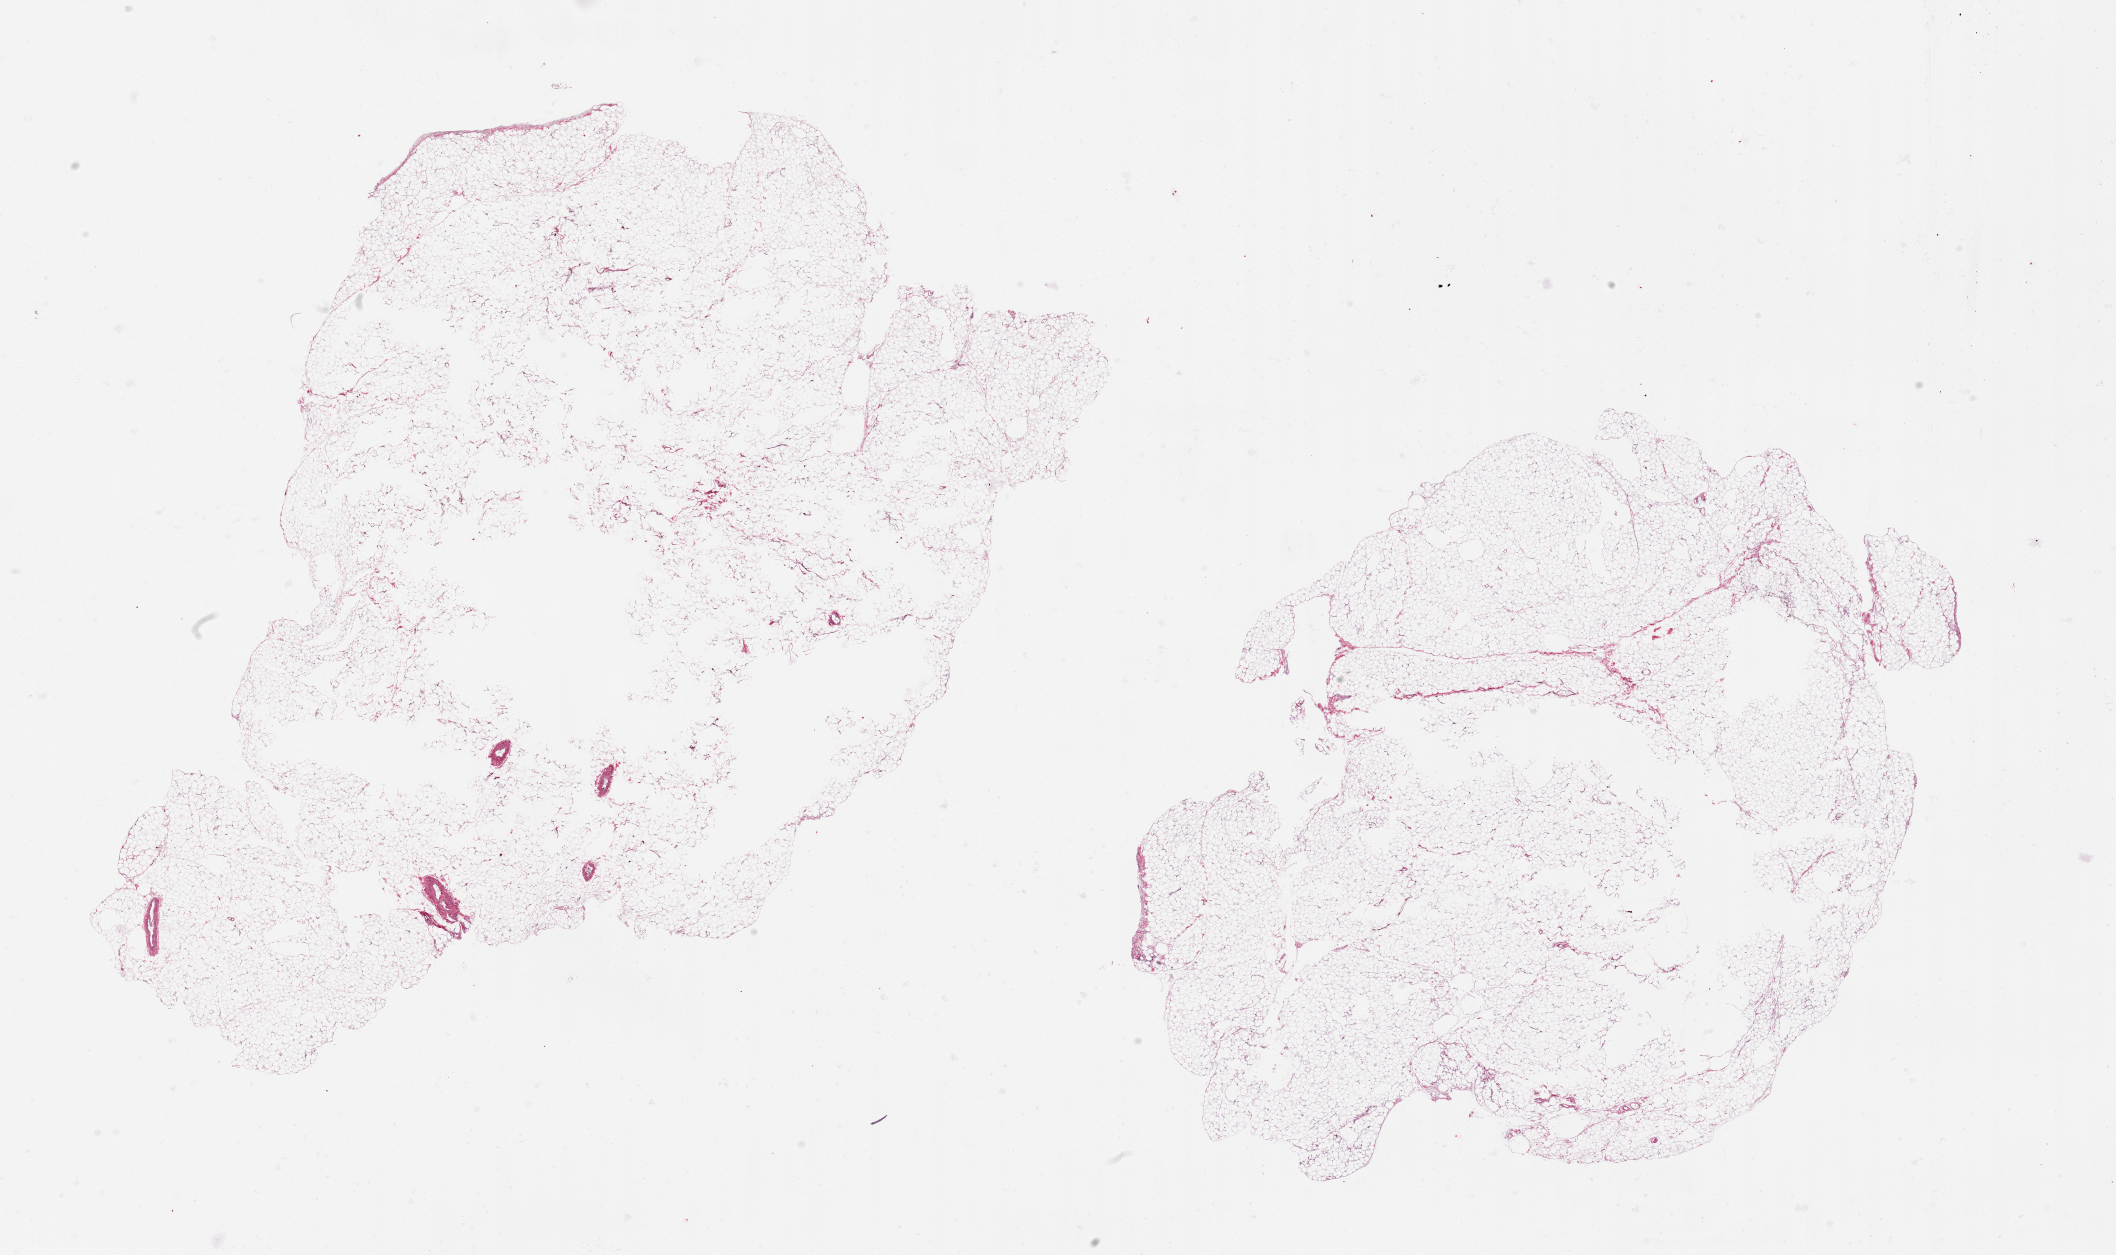
Digitized H&E-stained section, brightfield — low-resolution overview of the scanned area, about 33.5 x 19.9 mm (from a 20x scan). PAXgene-fixed, paraffin-embedded tissue. Section of omentum (target tissue). Tissue donor sample. Donor: male.
Reviewer comment on this tissue sample: 2 pieces, 17x11 and 14x10mm; over sized samples with central unfixed holes.